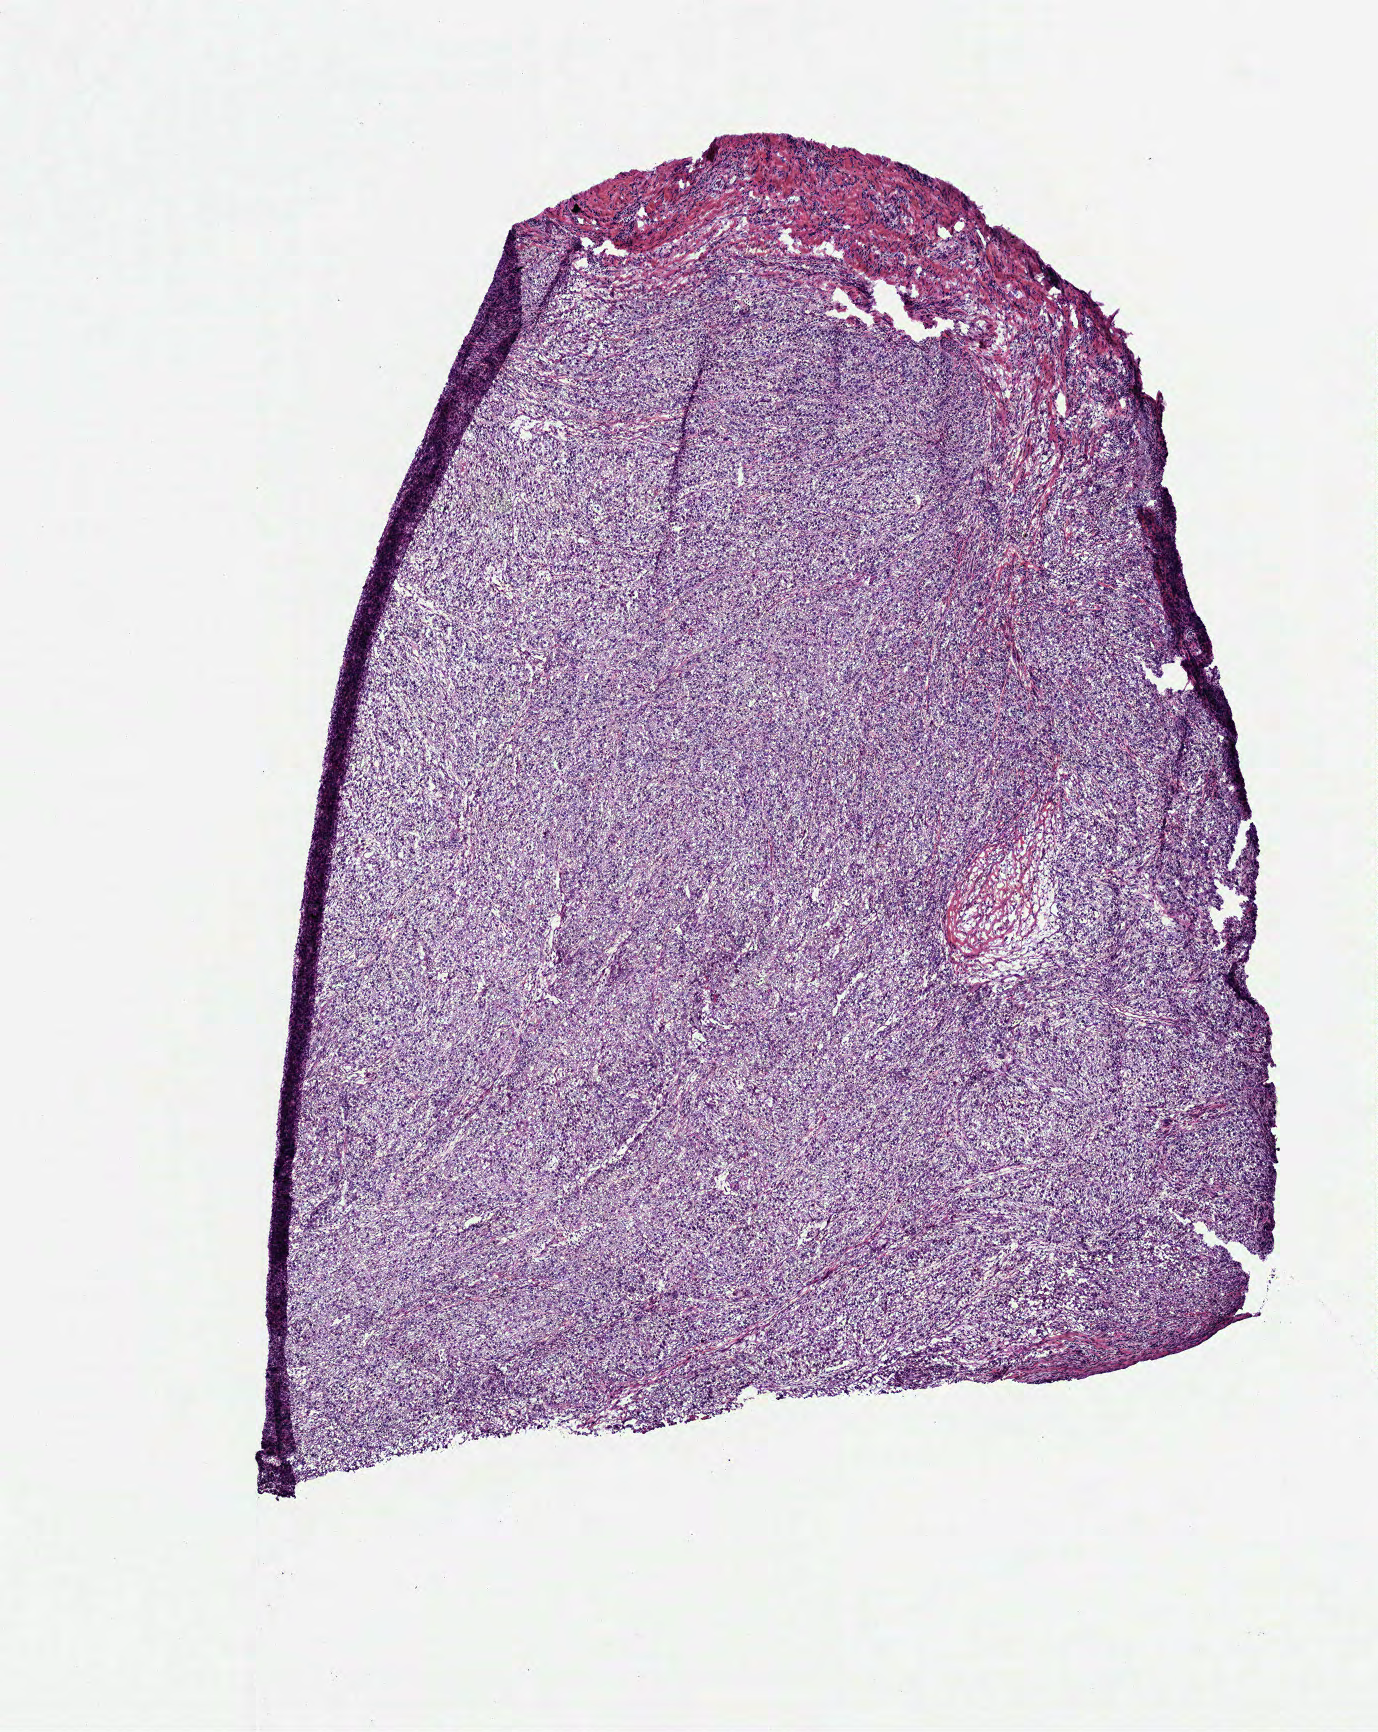
Whole-slide histology image, H&E-stained, shown as a low-resolution overview of the whole scanned area (about 5.6 x 7.0 mm); frozen section from the top of the tissue portion; head and neck, primary tumour sample. Male, age 57 years at initial diagnosis. Histologic grade: G3 (poorly differentiated). Pathologist review of this section (percent, as recorded): tumour cells 90%, tumour nuclei 80%, normal cells 0%, stromal cells 10%, necrosis 0%.
AJCC pathologic stage: IVA. Histologic diagnosis: Squamous cell carcinoma, NOS.